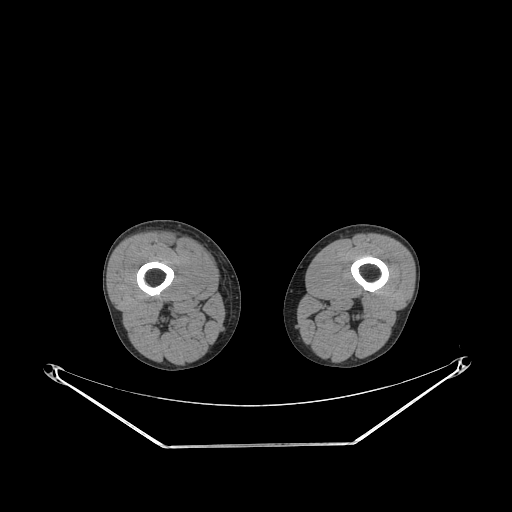
CT of an extremity soft-tissue mass (from a PET/CT study), one axial slice; position 223 of 311 along the scan axis; reconstruction kernel STANDARD; 140 kVp; soft-tissue window (W 400 / L 40 HU); 3.75 mm slice thickness; 512 × 512 image matrix. Male patient. Case-level facts recorded for this patient, not image findings: histological type: pleiomorphic leiomyosarcoma; grade: intermediate; site of the primary tumour: right thigh.
Annotated regions visible in this slice (expert contour drawn on MRI and transferred to this co-registered scan by the dataset authors):
- gross tumour volume including surrounding oedema: bounding box (x1, y1, x2, y2) in pixels: (165, 238, 175, 243)